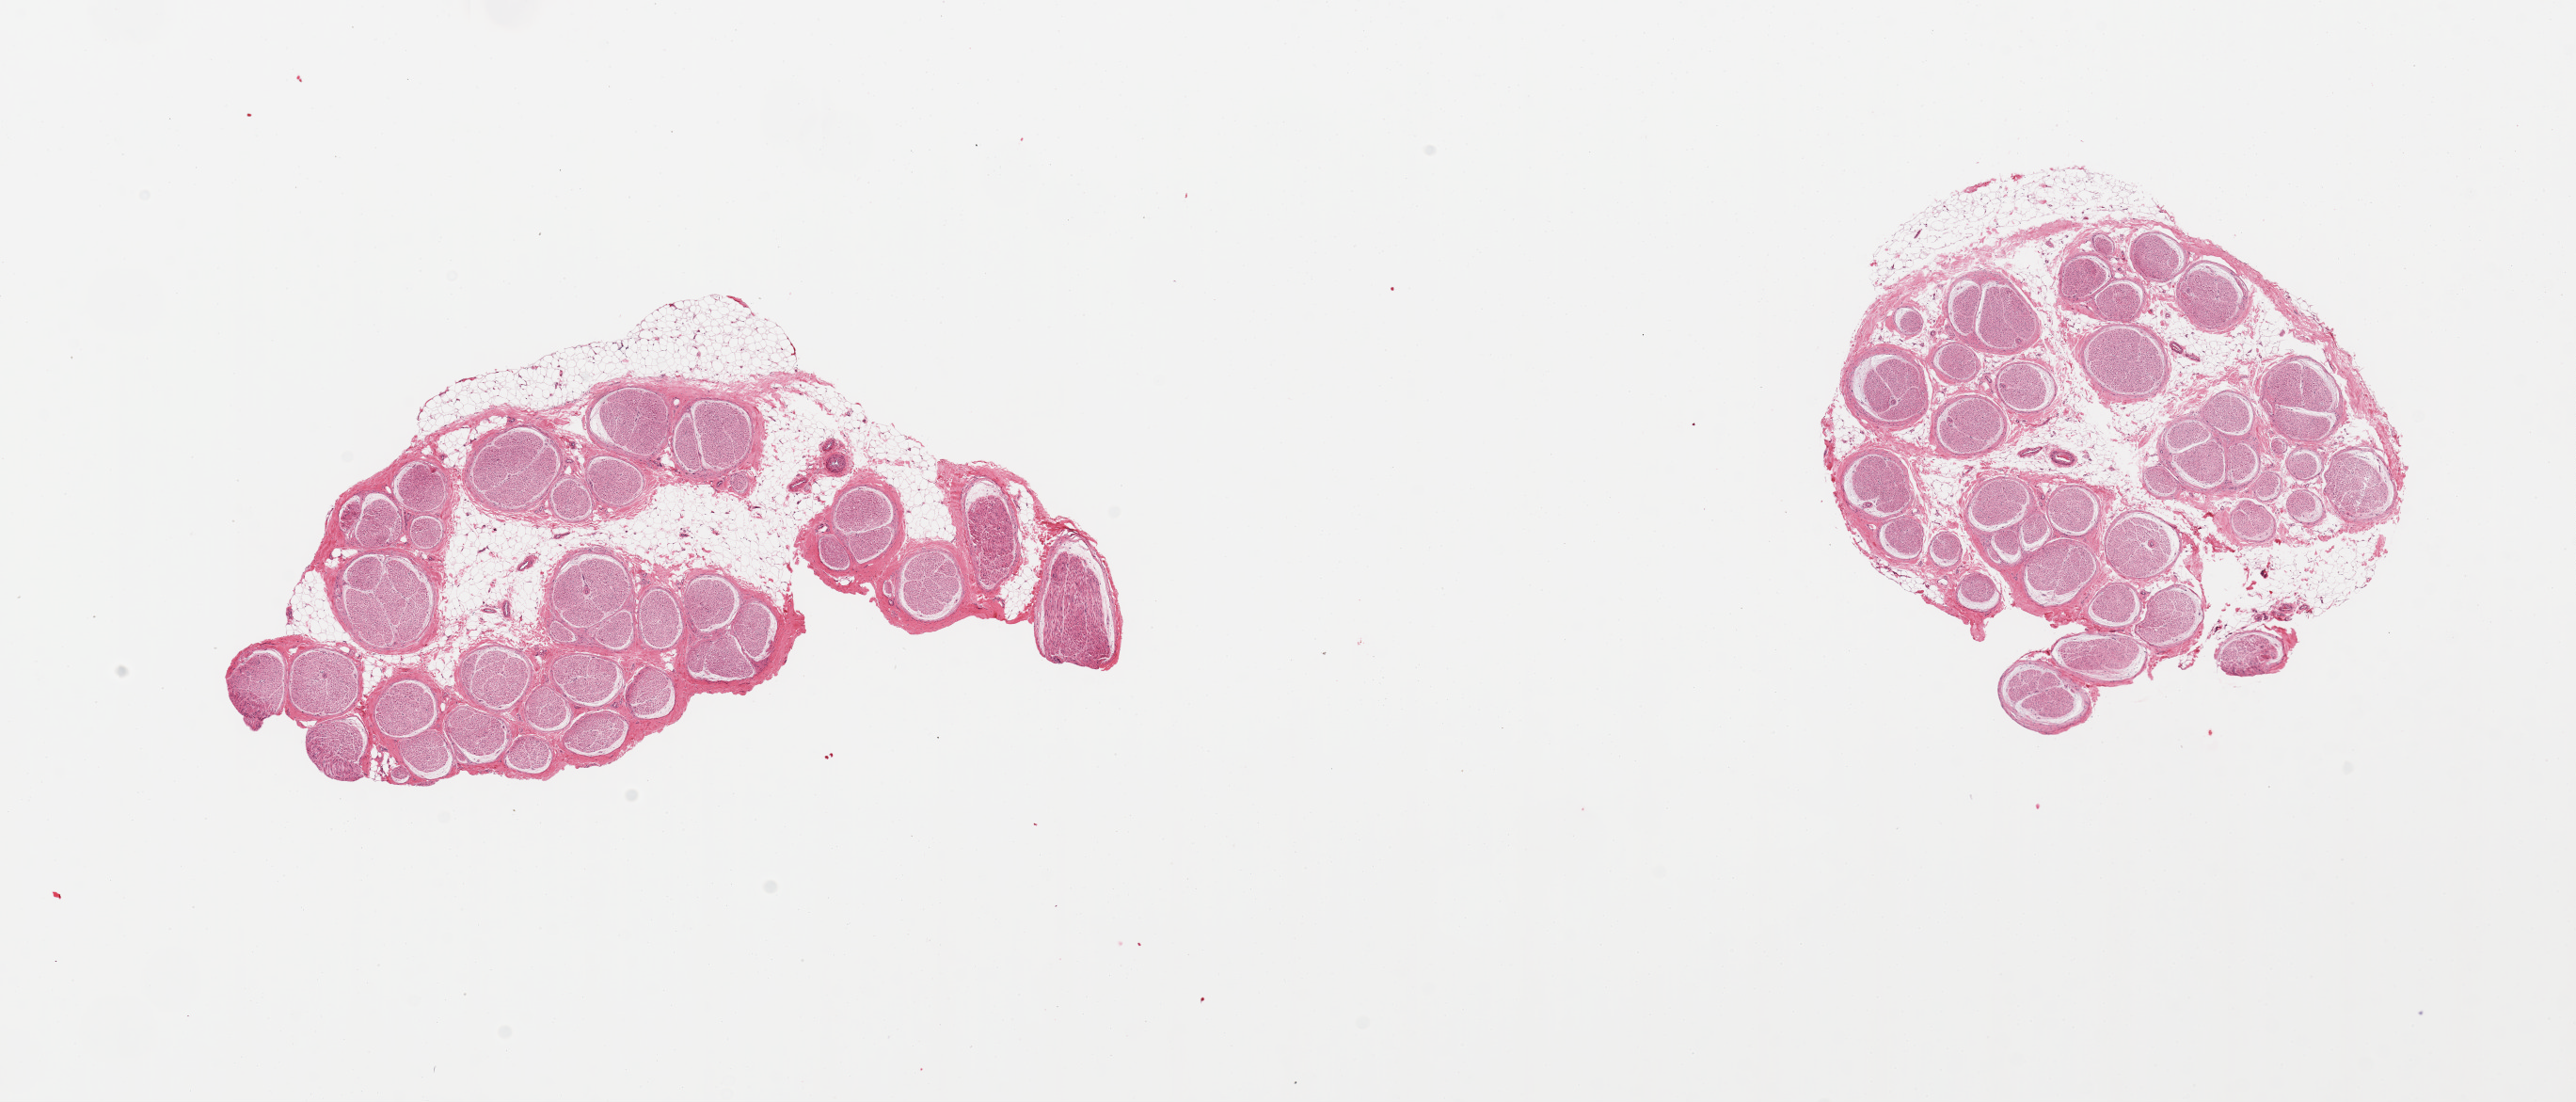
Whole-slide image, H&E stain — a low-resolution overview of the entire scanned area, about 21.7 x 9.3 mm (acquisition: 20x scan). PAXgene-fixed, paraffin-embedded tissue. Section of tibial nerve (target tissue). Donor tissue sample. Male donor.
* pathologist's review note for this sample: 2 pieces; attached and internal fat up to 25%